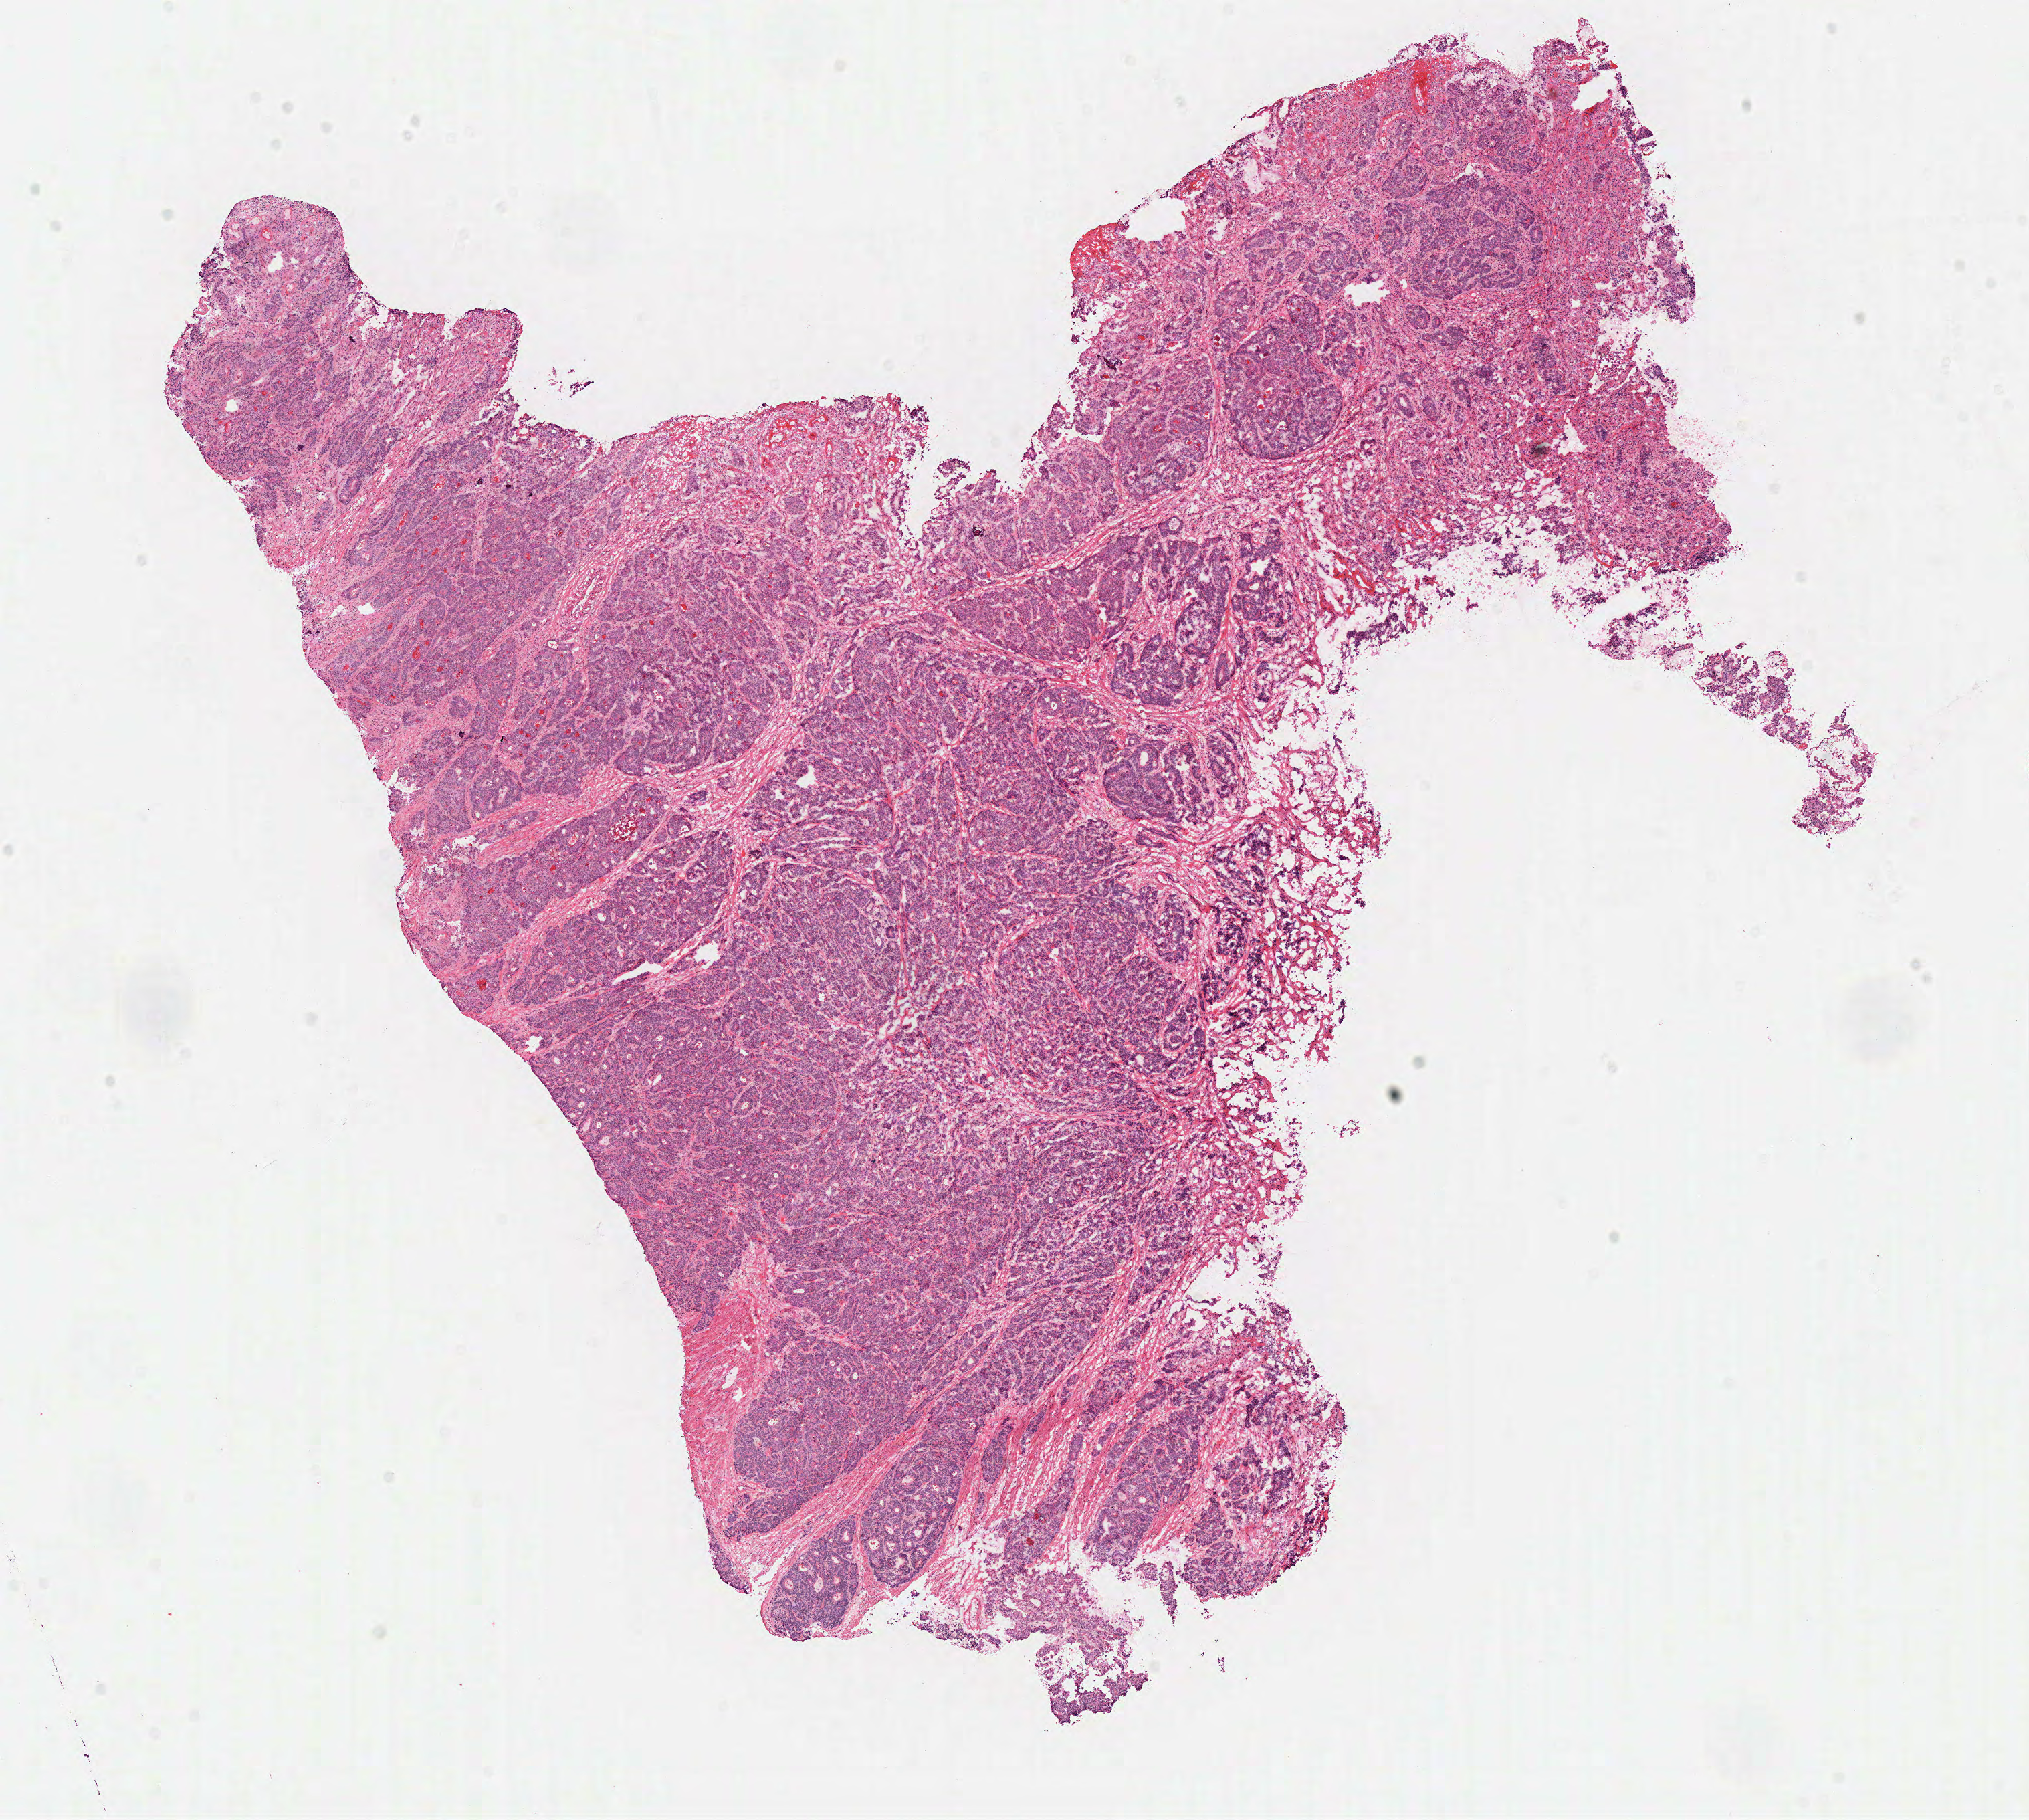
Whole-slide histology image, H&E-stained — low-resolution overview of the scanned area, about 12.0 x 10.7 mm (from a 40x scan); frozen section; sample: primary tumour, colon. Patient: male, age at initial diagnosis 80 years. Composition of this section per pathologist review: tumour cells 99%, tumour nuclei 90%, normal cells 0%, stromal cells 0%, necrosis 1%. Infiltration values recorded for this section: lymphocyte infiltration 2%, monocyte infiltration 0%, neutrophil infiltration 0%.
- pathologic diagnosis: Adenocarcinoma, NOS
- AJCC pathologic stage: IVA (7th edition)